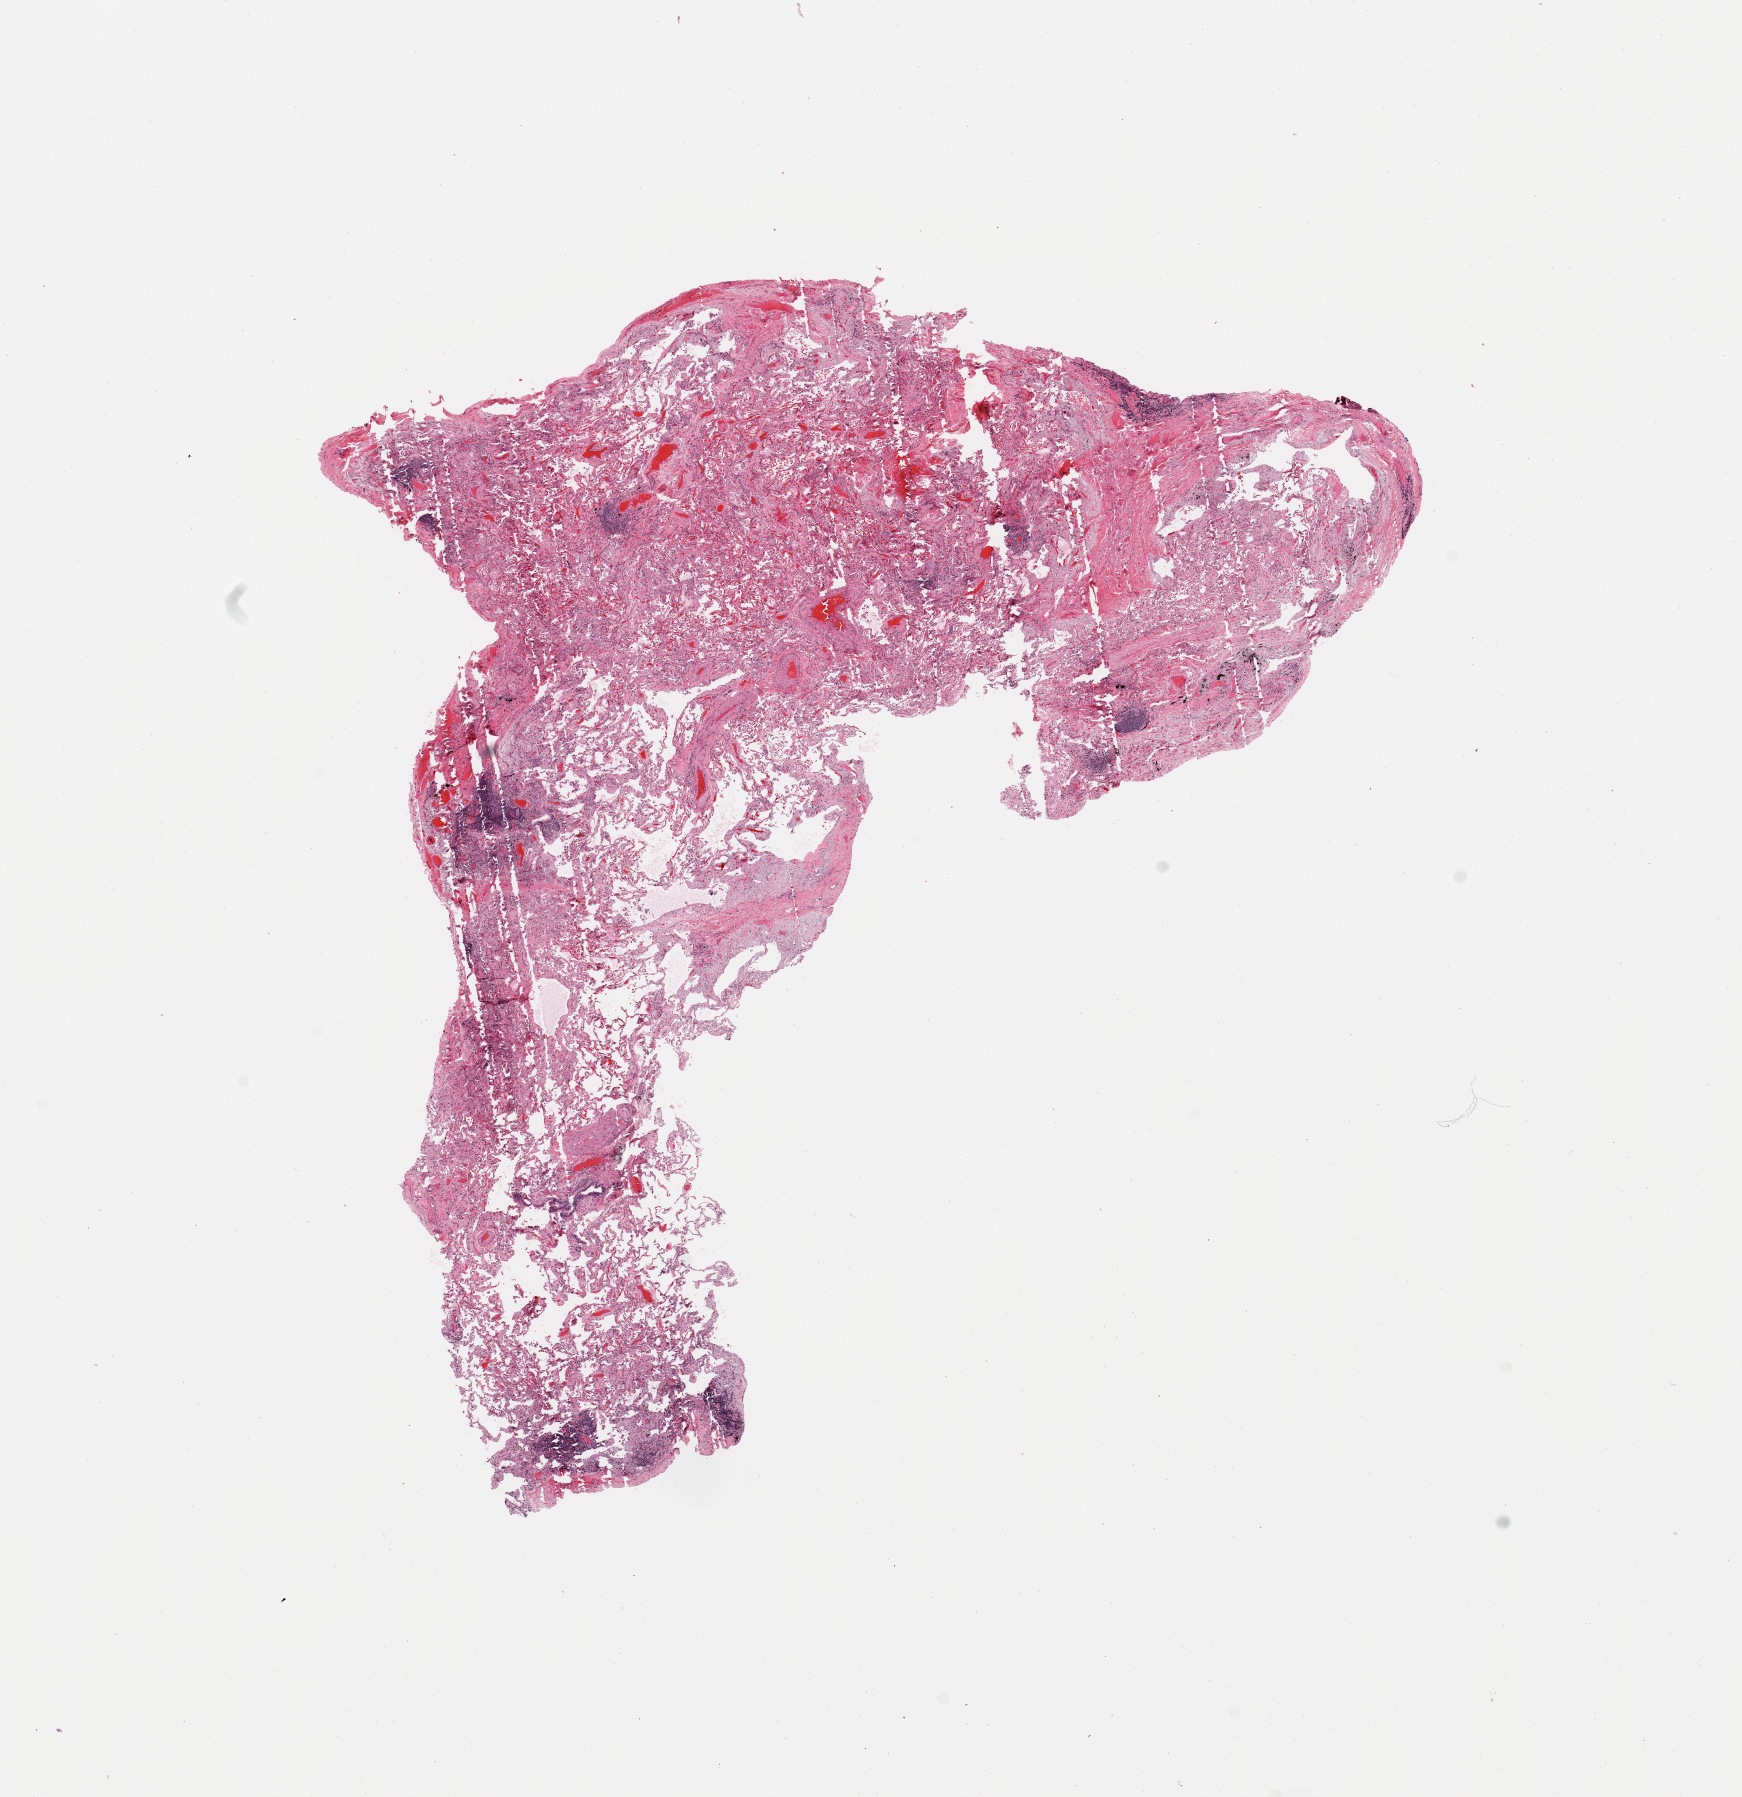
Digitized Hematoxylin and eosin (H&E) stained tissue section (whole slide) — whole scanned area (about 13.8 x 14.2 mm, slide scanned at 20x) shown as a low-resolution overview, normal (non-tumour) tissue sample, sampled site: lung. 74-year-old male patient.
This section: normal (non-tumour) tissue from the same patient. Patient diagnosis: Squamous cell carcinoma, NOS.